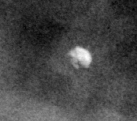
Crop from a digitized film mammogram around one marked abnormality; right breast; MLO view; BI-RADS breast density category 3 (scale 1–4).
Finding: calcifications, morphology round and regular / lucent centered; BI-RADS assessment category 2; benign; no additional work-up was recommended (benign without callback).